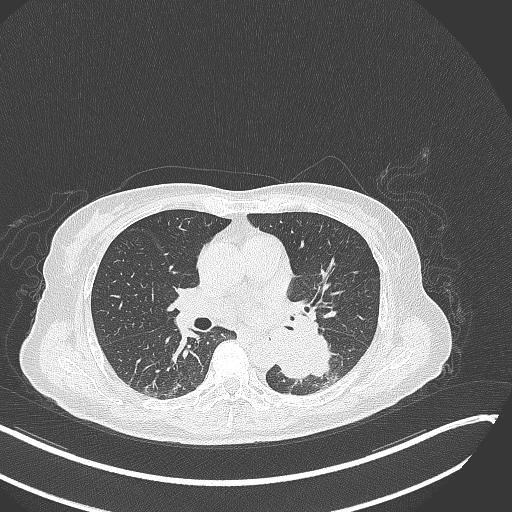
Chest CT, one axial slice; slice 147 of 342 in the series (ordered by position); reconstruction kernel B70f; 120 kVp; lung window (W 1500 / L -600 HU); 512 × 512 image matrix. Female patient, age 64 years. Case-level facts recorded for this patient, not image findings: clinical TNM (as recorded): T3 N1 M1; histopathological grade: G3.
Structures marked on this image (bounding box drawn by a radiologist):
- lung tumour (recorded histology: small cell carcinoma): bounding box [x1, y1, x2, y2] px = [270, 326, 337, 384]